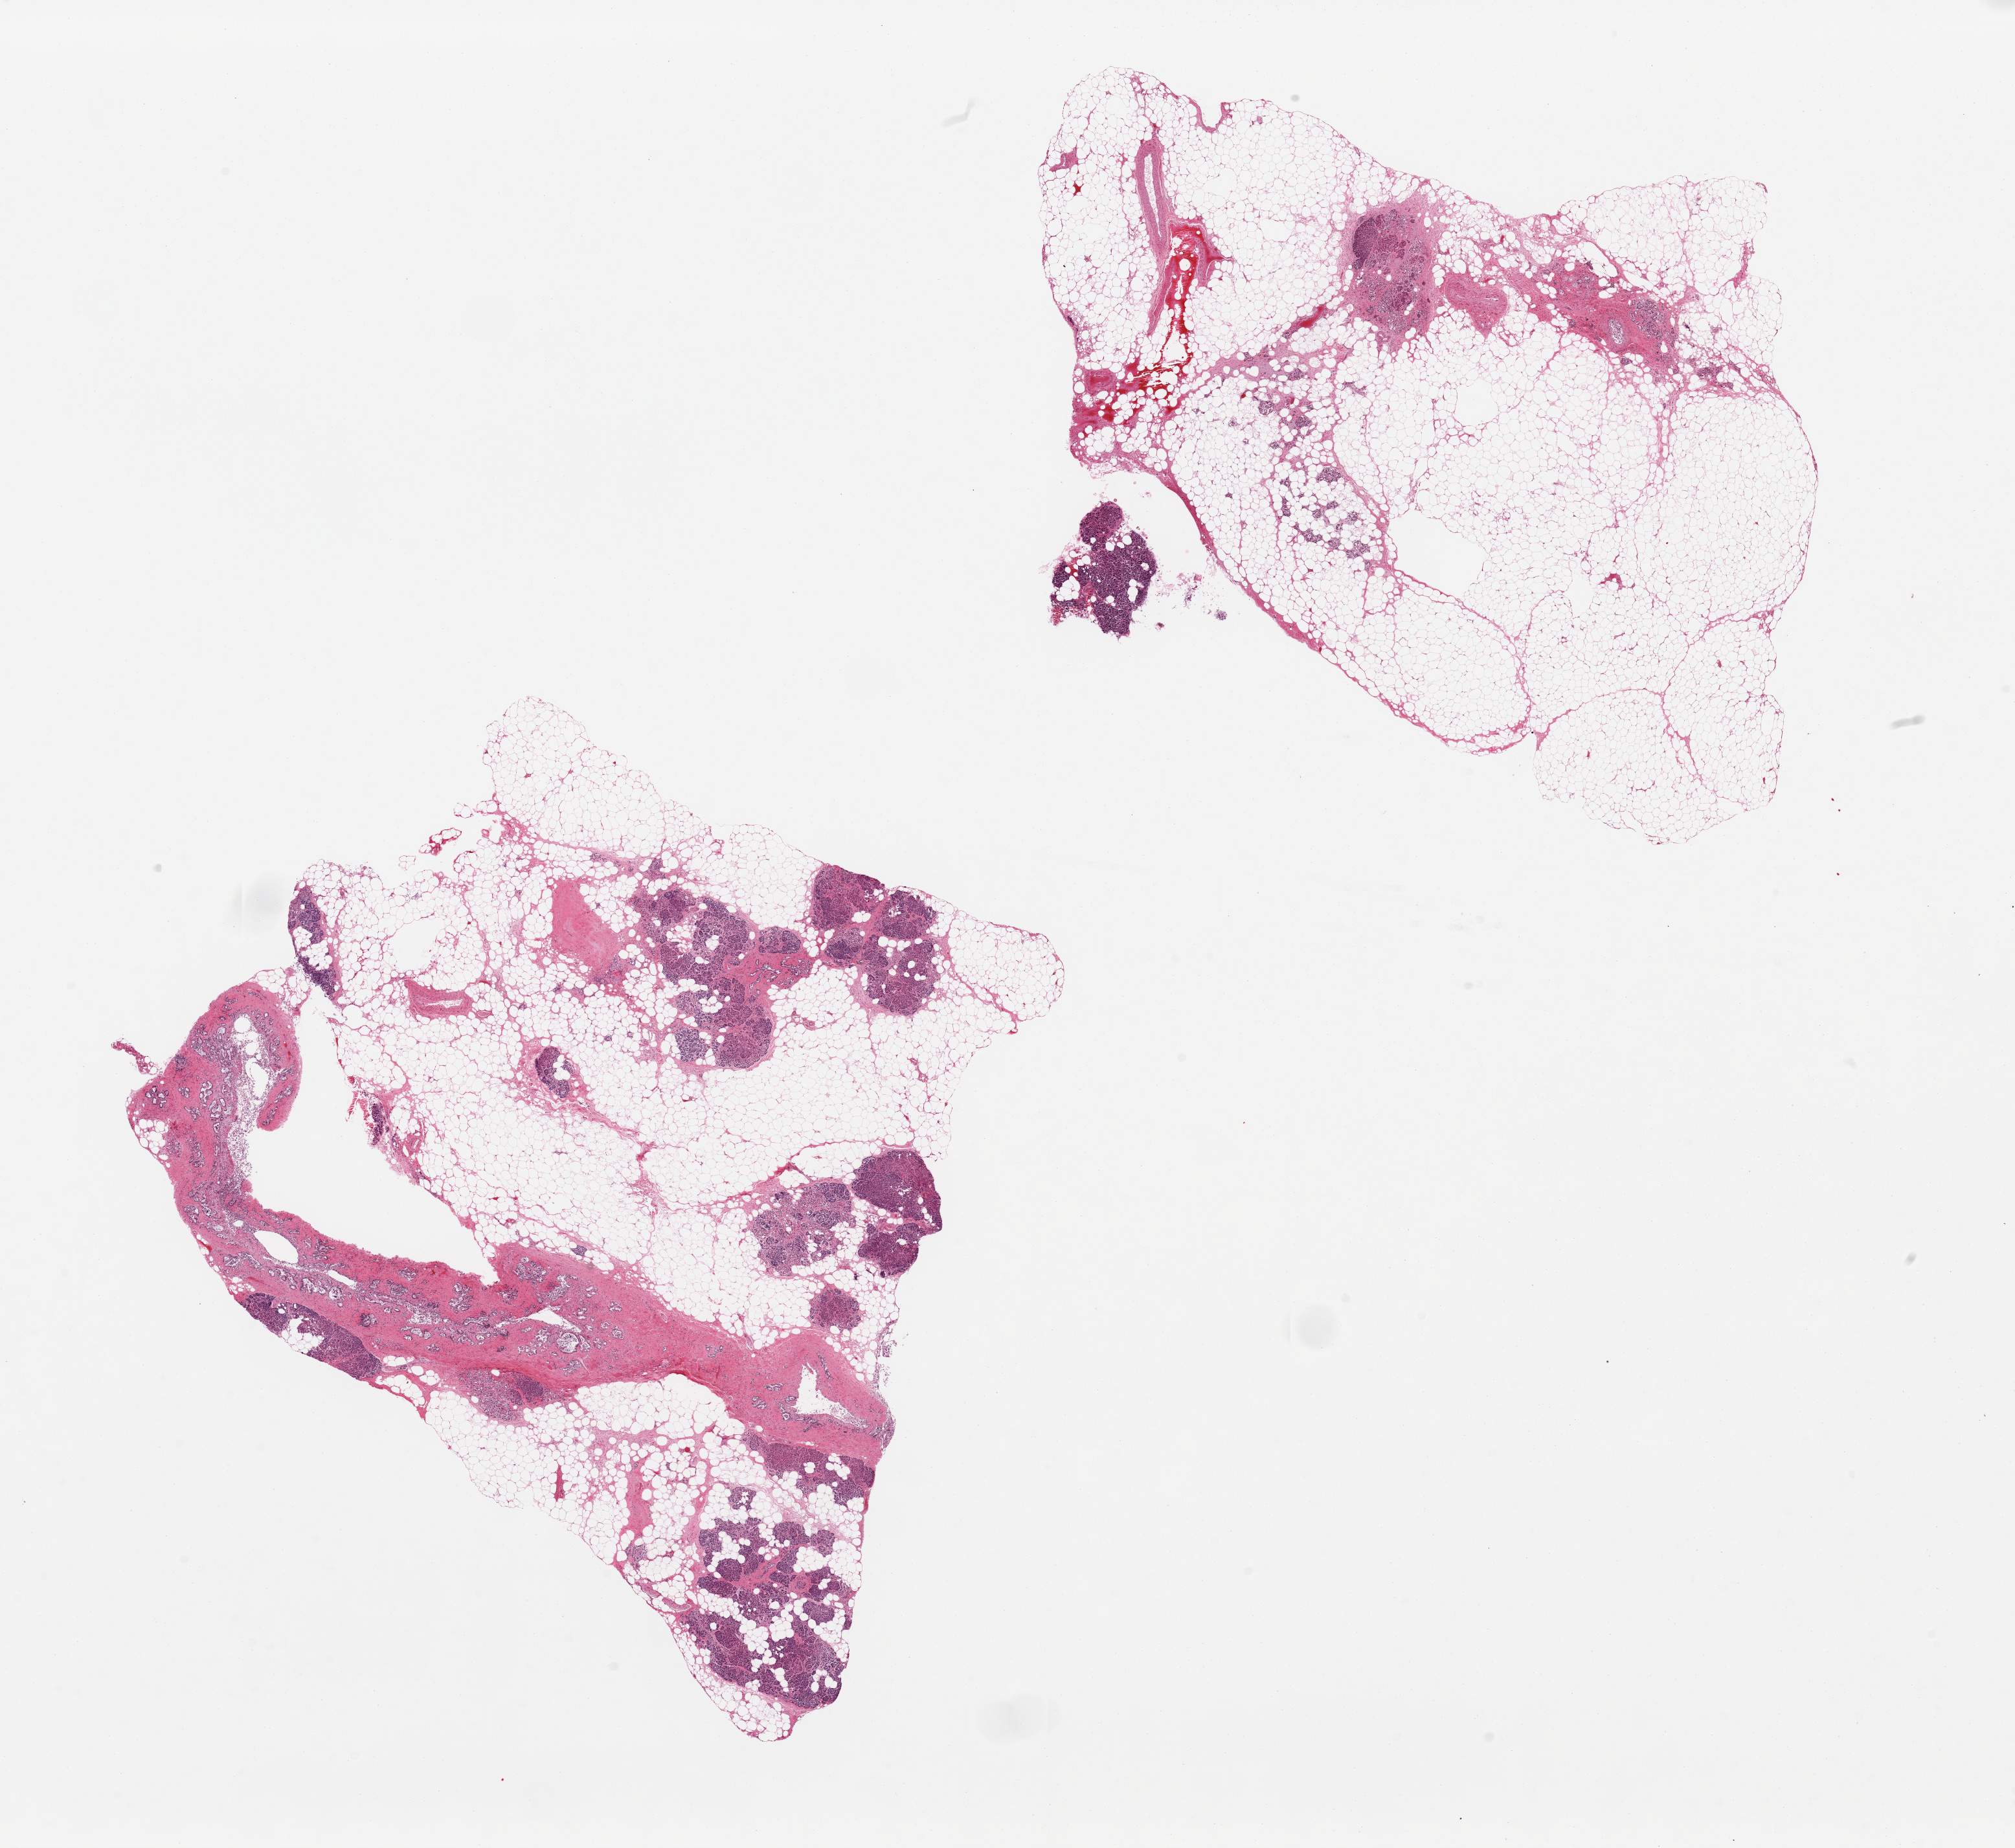
Whole-slide image, H&E stain — low-resolution overview of the scanned area, about 24.6 x 22.6 mm. PAXgene-fixed, paraffin-embedded tissue. Target tissue: pancreas. Tissue donor sample. Donor sex: male.
Reviewer comment on this tissue sample: 2 pieces, predominantly fat with limited parenchyma, fibrosis and atrophy, proliferation of ducts with sloughed lining, ?PanIN.